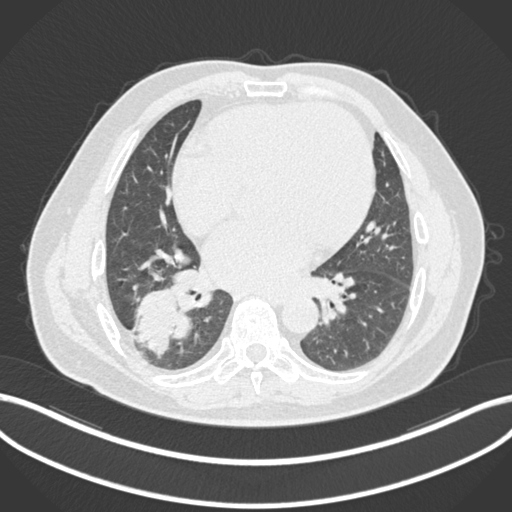
Chest CT, one axial slice. Slice 74 of 200 in the series (ordered by position). Reconstruction kernel B30f. Lung window (W 1500 / L -600 HU). 512 × 512 image matrix, field of view 400 × 400 mm. Patient: male, 59 years.
Annotated regions visible in this slice (bounding box drawn by a radiologist):
- lung tumour (recorded histology: adenocarcinoma): bounding box <129,291,194,359> (left, top, right, bottom; pixels)